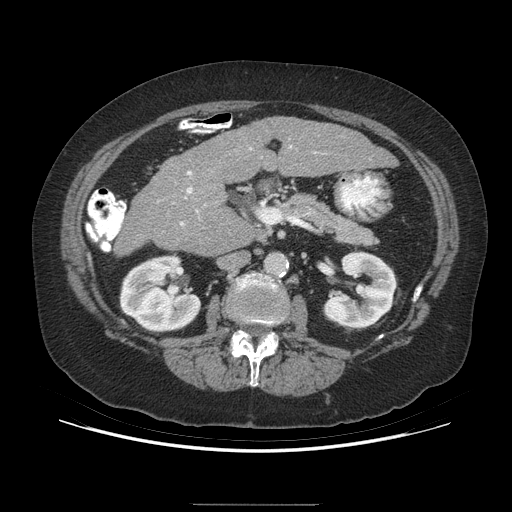
Contrast-enhanced abdominal CT (liver protocol), one axial slice. Position 141 of 192 along the scan axis. Reconstruction kernel STANDARD. 140 kVp. Soft-tissue window (W 400 / L 40 HU). 2.5 mm slice thickness. 512 × 512 image matrix. From the clinical record (not read from this slice): diagnosis: hepatocellular carcinoma (patient treated with transarterial chemoembolisation; whether this scan precedes or follows treatment is not stated here); TNM stage (as recorded): Stage-I; Child-Pugh class: A; tumour differentiation: moderately differentiated; tumour nodularity: uninodular.
Structures marked on this image (semi-automatic segmentation, software-assisted and operator-edited):
- liver parenchyma outside the tumour (the mass and vessels are separate outlines, so this box may not span the whole liver): bounding box (x1, y1, x2, y2) in pixels: (114, 116, 396, 254)
- liver vessels: (180, 148, 251, 225)